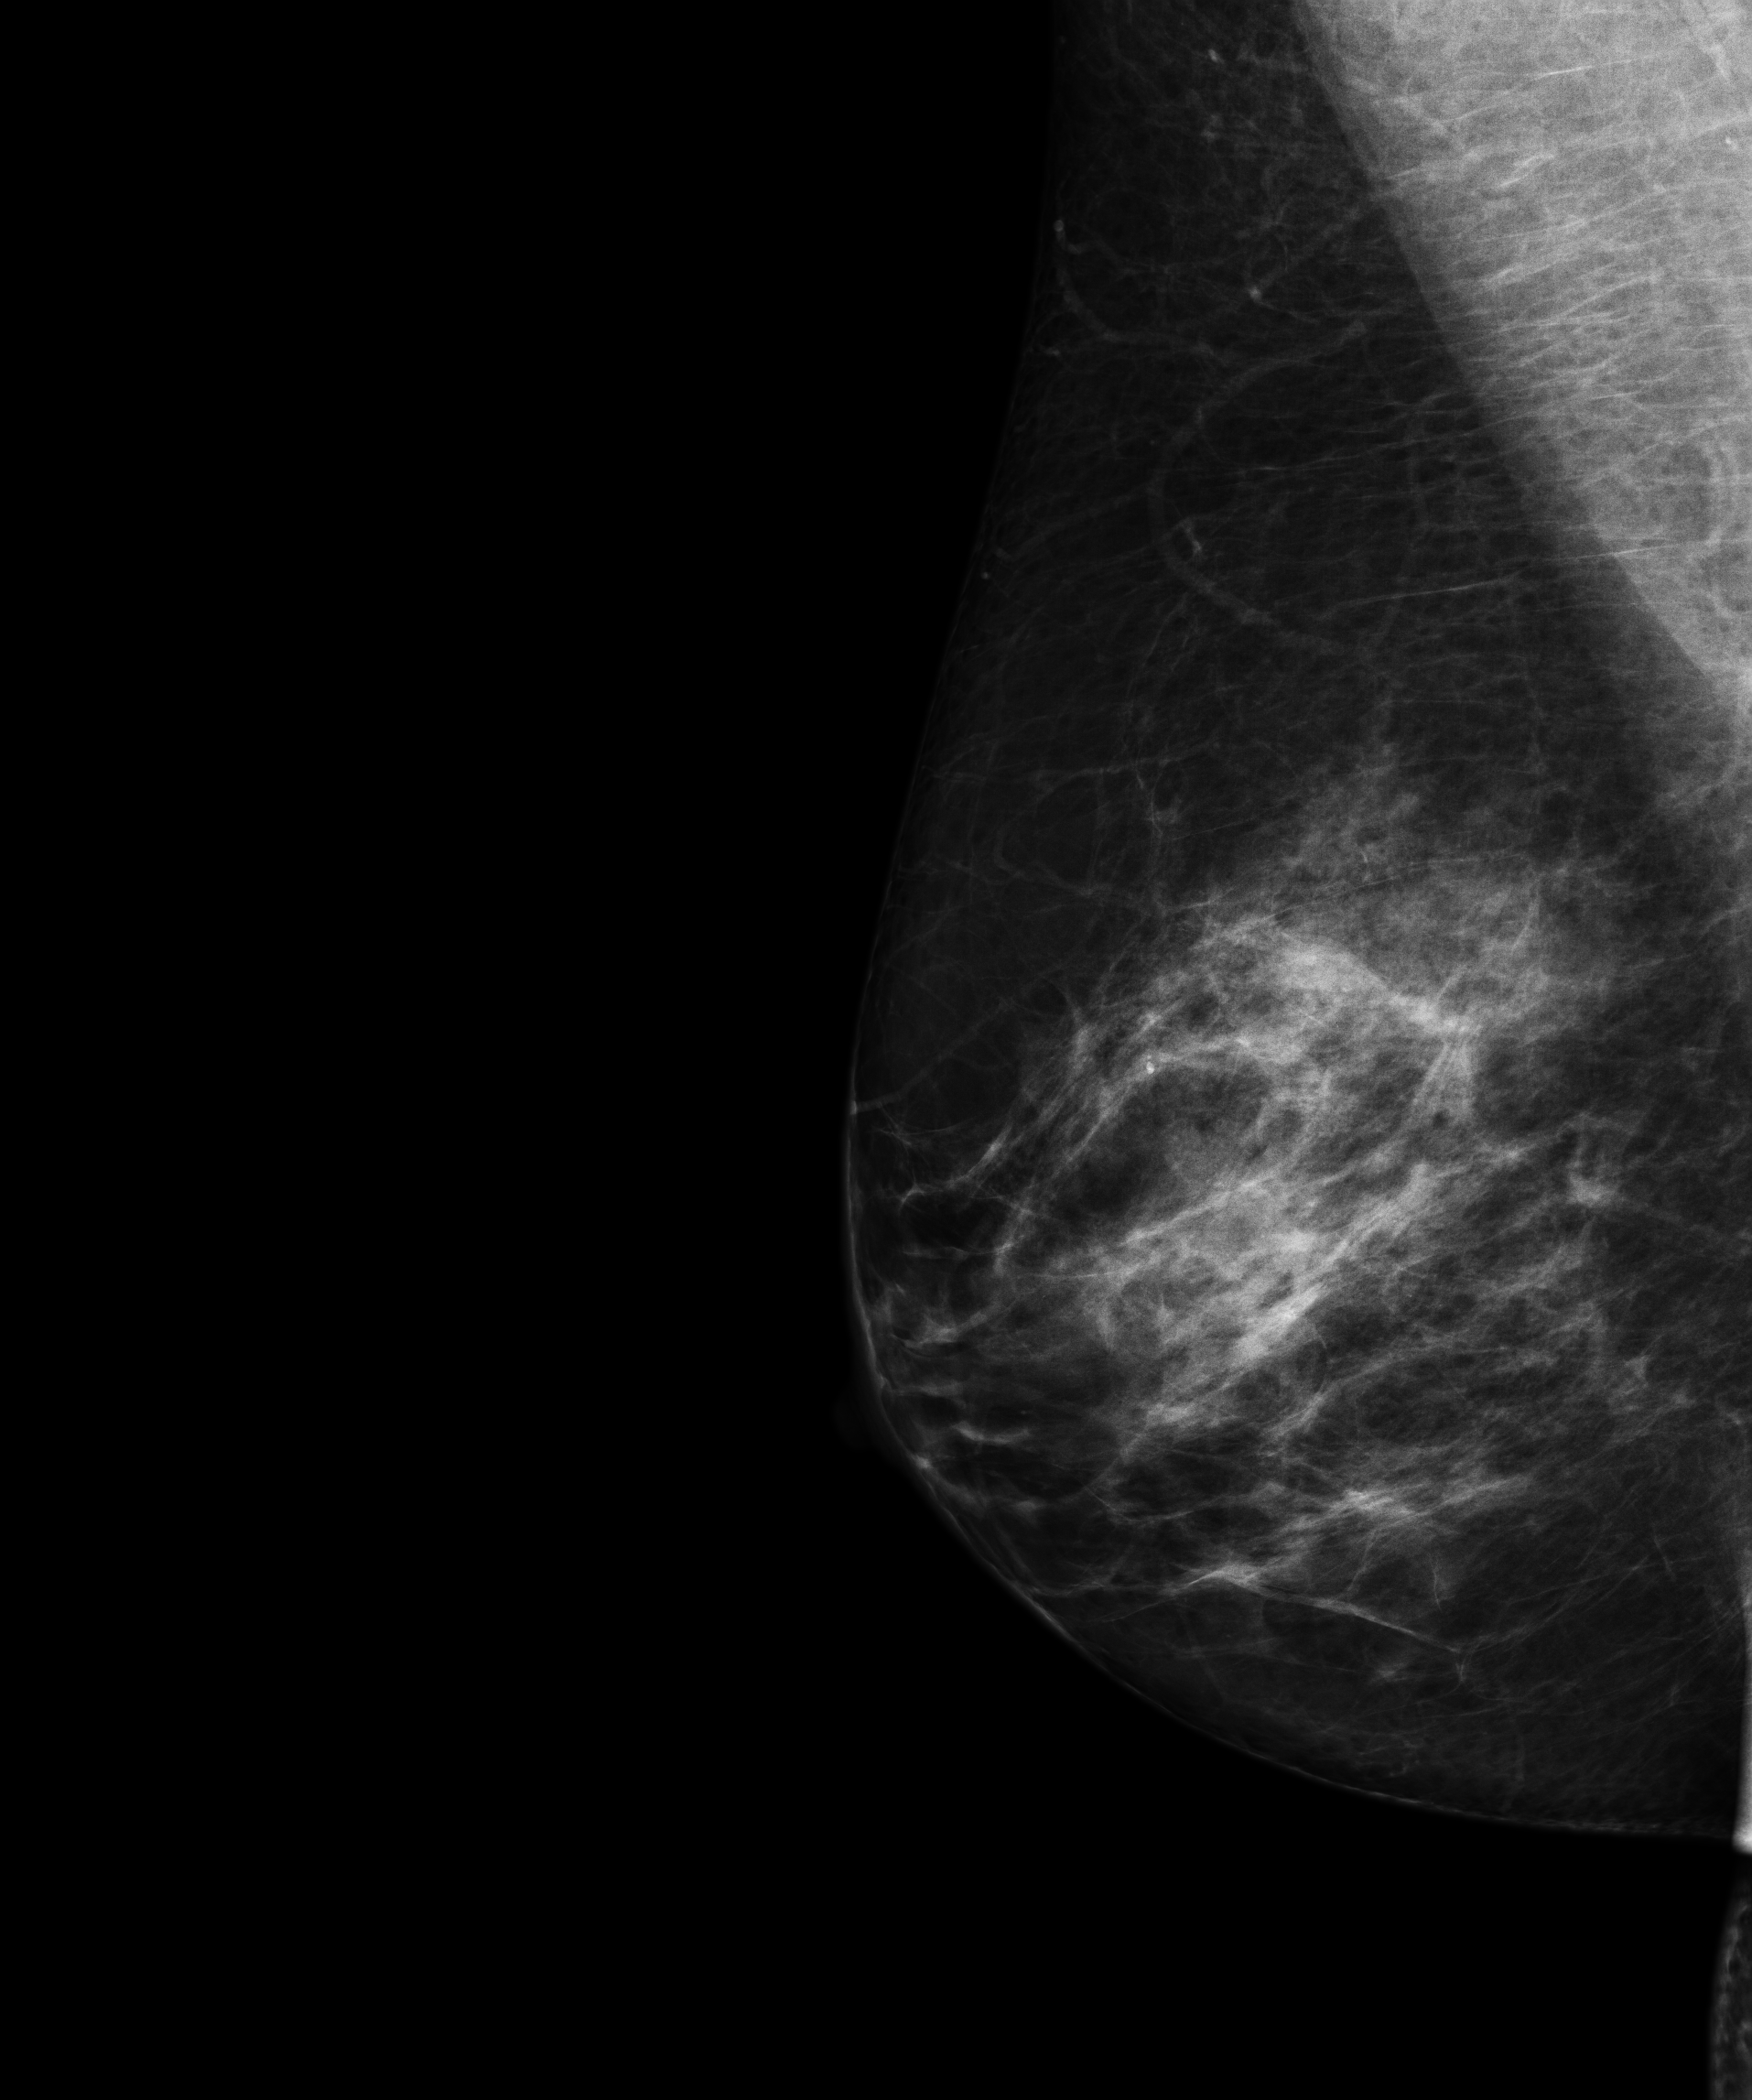
Full-field digital mammogram (FFDM); right breast; medio-lateral oblique projection; annual screening mammography examination; compressed breast thickness 68 mm; system: Senographe Essential ADS_56.21.3. Patient: female, 45 years.
Breast density at the screening exam (both breasts): heterogeneously dense (BI-RADS density category c). Final BI-RADS assessment for this screening round (tomosynthesis exam, both breasts): category 1. Recall: no recall after this screen.